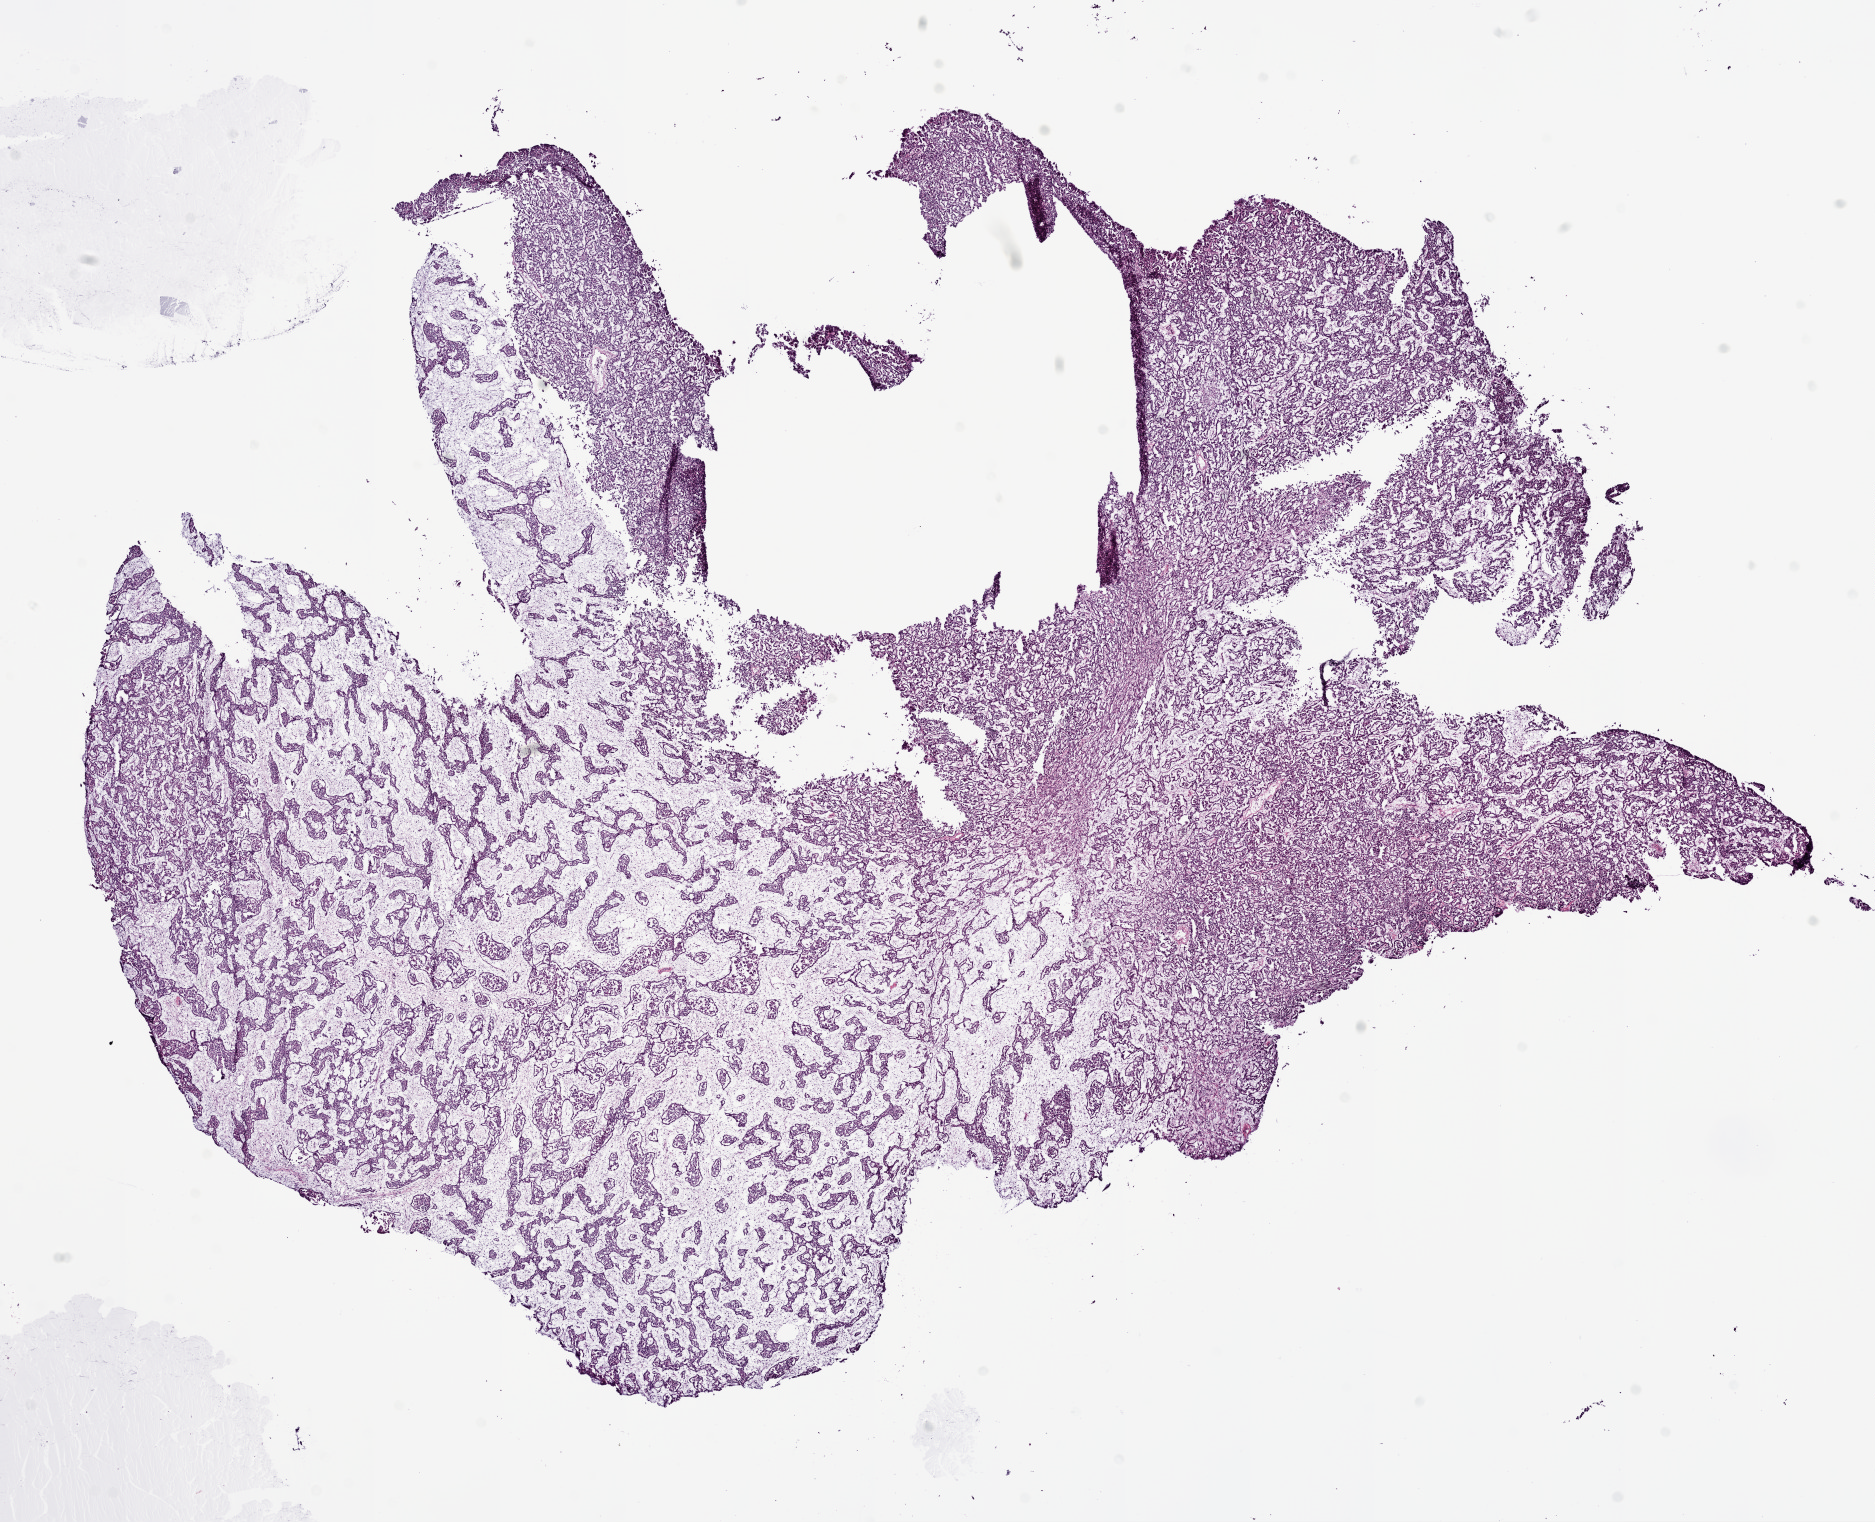
Whole-slide histology image, H&E-stained — shown as a low-resolution overview of the whole scanned area (about 15.0 x 12.2 mm, slide scanned at 20x); frozen section from the bottom of the tissue portion; kidney, primary tumour sample. Female, age 38 years at initial diagnosis. Pathologist review of this section (percent, as recorded): tumour cells 70%, tumour nuclei 80%, normal cells 0%, stromal cells 30%, necrosis 0%.
AJCC pathologic stage: I (6th edition). Pathologic diagnosis: Papillary adenocarcinoma, NOS. Laterality: right.